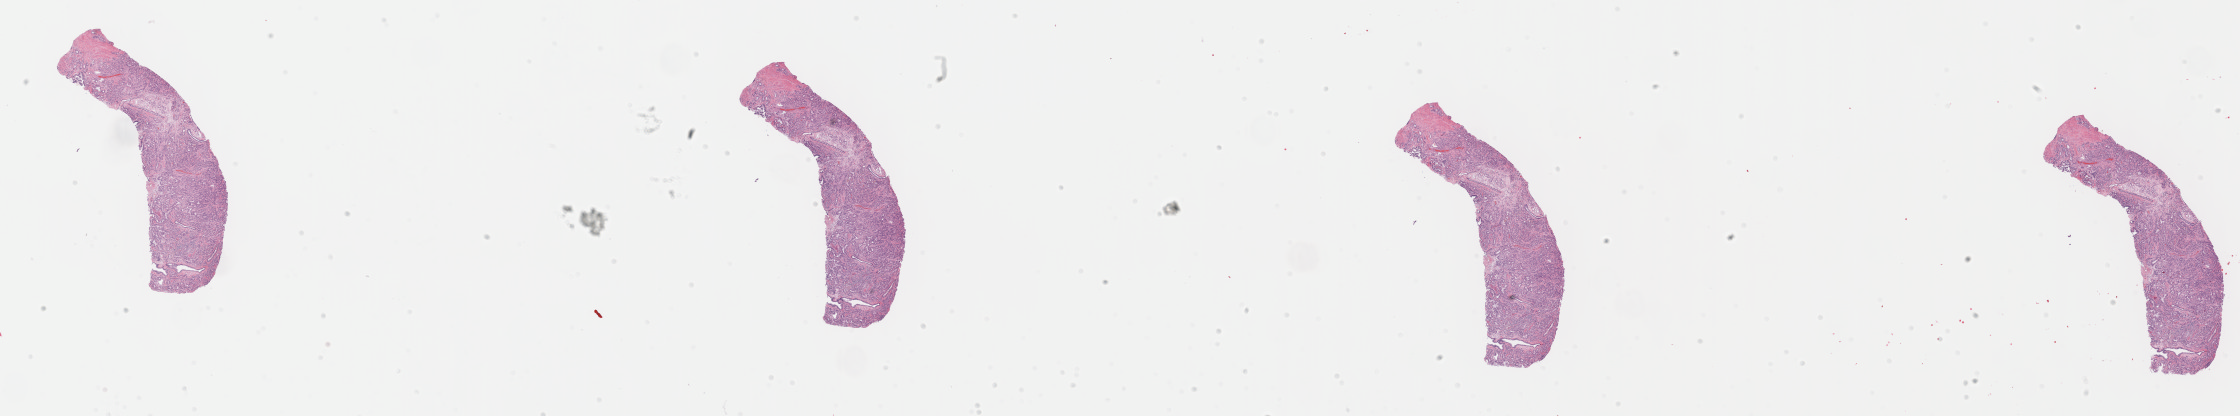
Digitized Hematoxylin and eosin (H&E) stained tissue section (whole slide) — low-resolution overview of the scanned area, about 36.2 x 6.7 mm. Formalin-fixed paraffin-embedded (FFPE) diagnostic section. Sample: primary tumour, prostate. Male patient; age at initial diagnosis 62 years. Gleason score: 7 (4+3). Composition of this section per pathologist review: tumour cells 57%, tumour nuclei 90%, normal cells 2%, stromal cells 40%, necrosis 1%. Infiltration values recorded for this section: lymphocyte infiltration 3%, monocyte infiltration 0%, neutrophil infiltration 0%.
Lymph nodes positive (case pathology): 0 of 6 examined. Diagnosis: Adenocarcinoma, NOS (prostate gland).